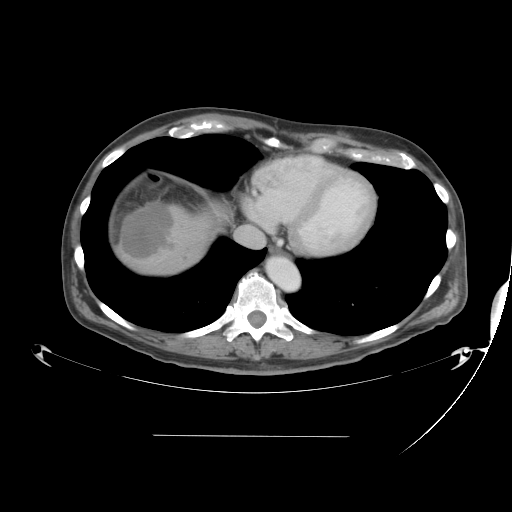
Contrast-enhanced abdominal CT, one axial slice. Slice 40 of 48 in the series (ordered by position). Reconstruction kernel STANDARD. Intravenous contrast given. Soft-tissue window (W 400 / L 40 HU). 5 mm slice thickness. 512 × 512 image matrix, field of view 486 × 486 mm. Male patient, age 65 years. Case-level facts recorded for this patient, not image findings: diagnosis: colorectal cancer liver metastases, imaged before liver resection; multiple liver metastases: yes; largest metastasis: 11 cm; disease in both lobes: yes.
Structures marked on this image (expert manual segmentation):
- liver: box from (x=119, y=202) to (x=210, y=280) px
- liver metastasis: (x=121, y=204)–(x=173, y=259)